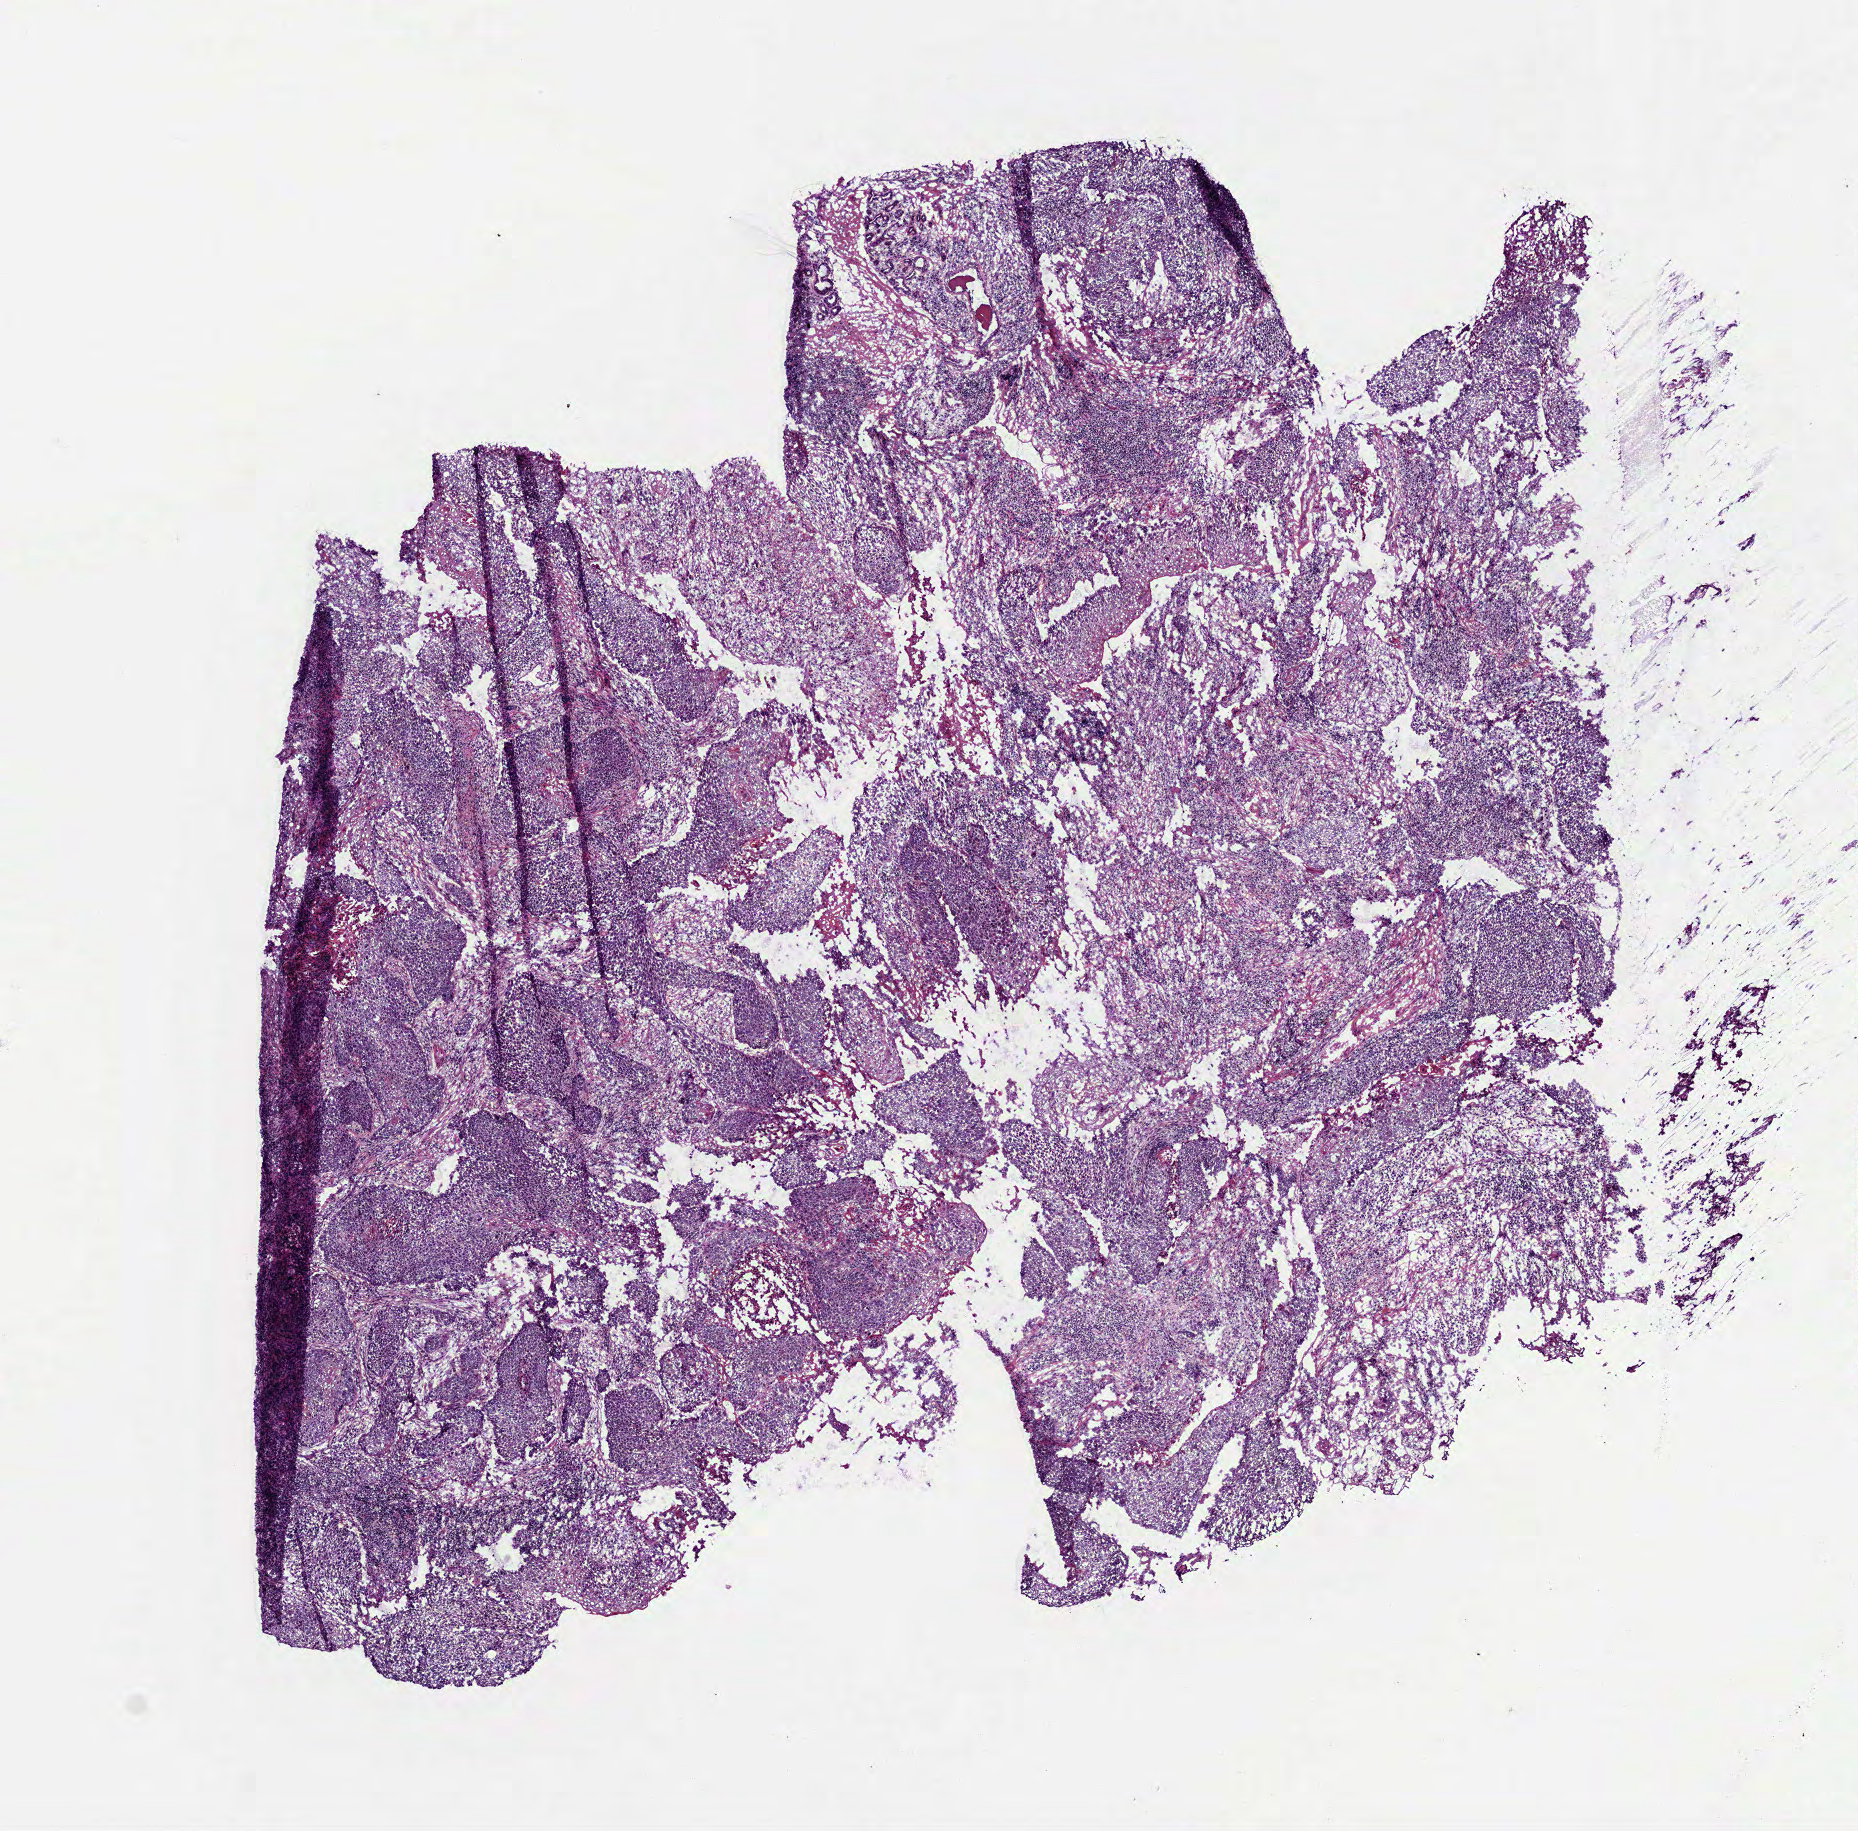
Whole-slide histology image, Hematoxylin and eosin (H&E) stained — low-resolution overview of the scanned area, about 7.5 x 7.4 mm. Frozen section from the bottom of the tissue portion. Head and neck, primary tumour sample. Patient: male, age at initial diagnosis 66 years. Histologic grade: G2 (moderately differentiated). Pathologist review of this section (percent, as recorded): tumour cells 80%, tumour nuclei 80%, normal cells 0%, stromal cells 15%, necrosis 5%.
* TNM: T3 N2c
* pathologic diagnosis: Squamous cell carcinoma, NOS (larynx, NOS)
* AJCC pathologic stage: IVA (7th edition)